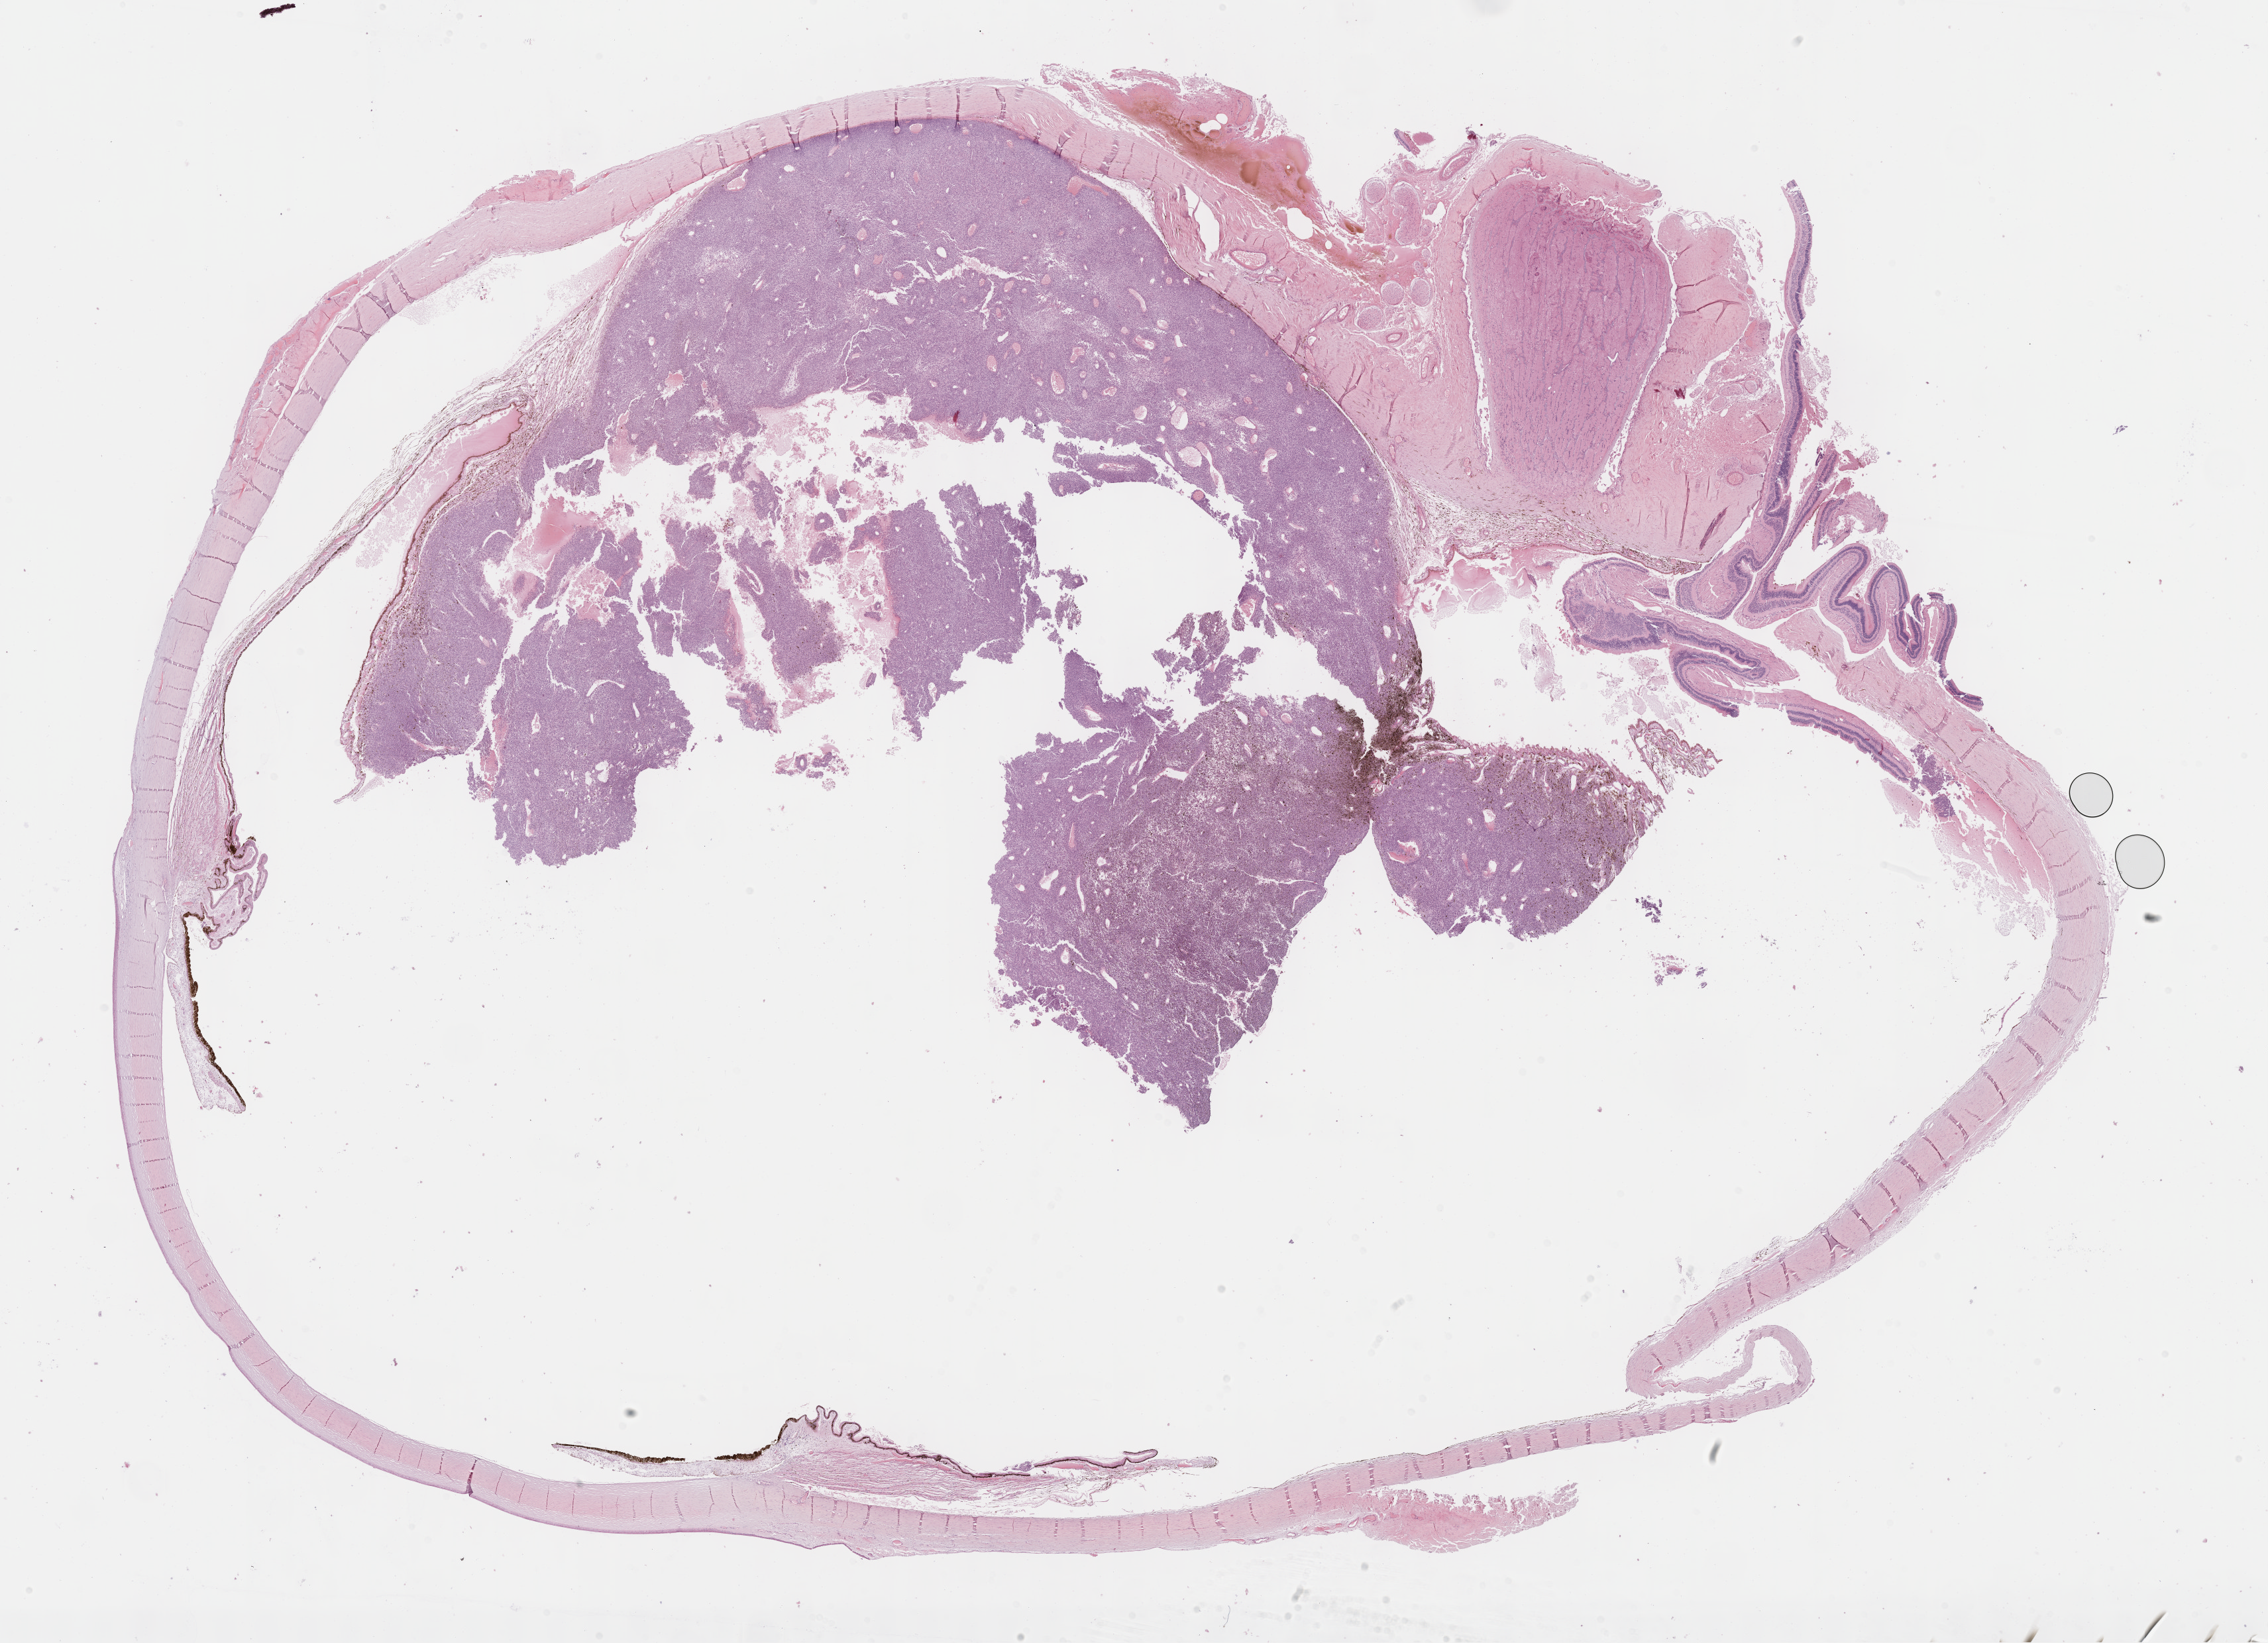
Digitized H&E-stained tissue section (whole slide), whole scanned area (about 27.7 x 20.1 mm) shown as a low-resolution overview; formalin-fixed paraffin-embedded (FFPE) diagnostic section; sample: primary tumour, uvea. Male patient; age at initial diagnosis 41 years.
Laterality: right. Histologic diagnosis: Mixed epithelioid and spindle cell melanoma (choroid). AJCC pathologic stage: IIIA (7th edition).